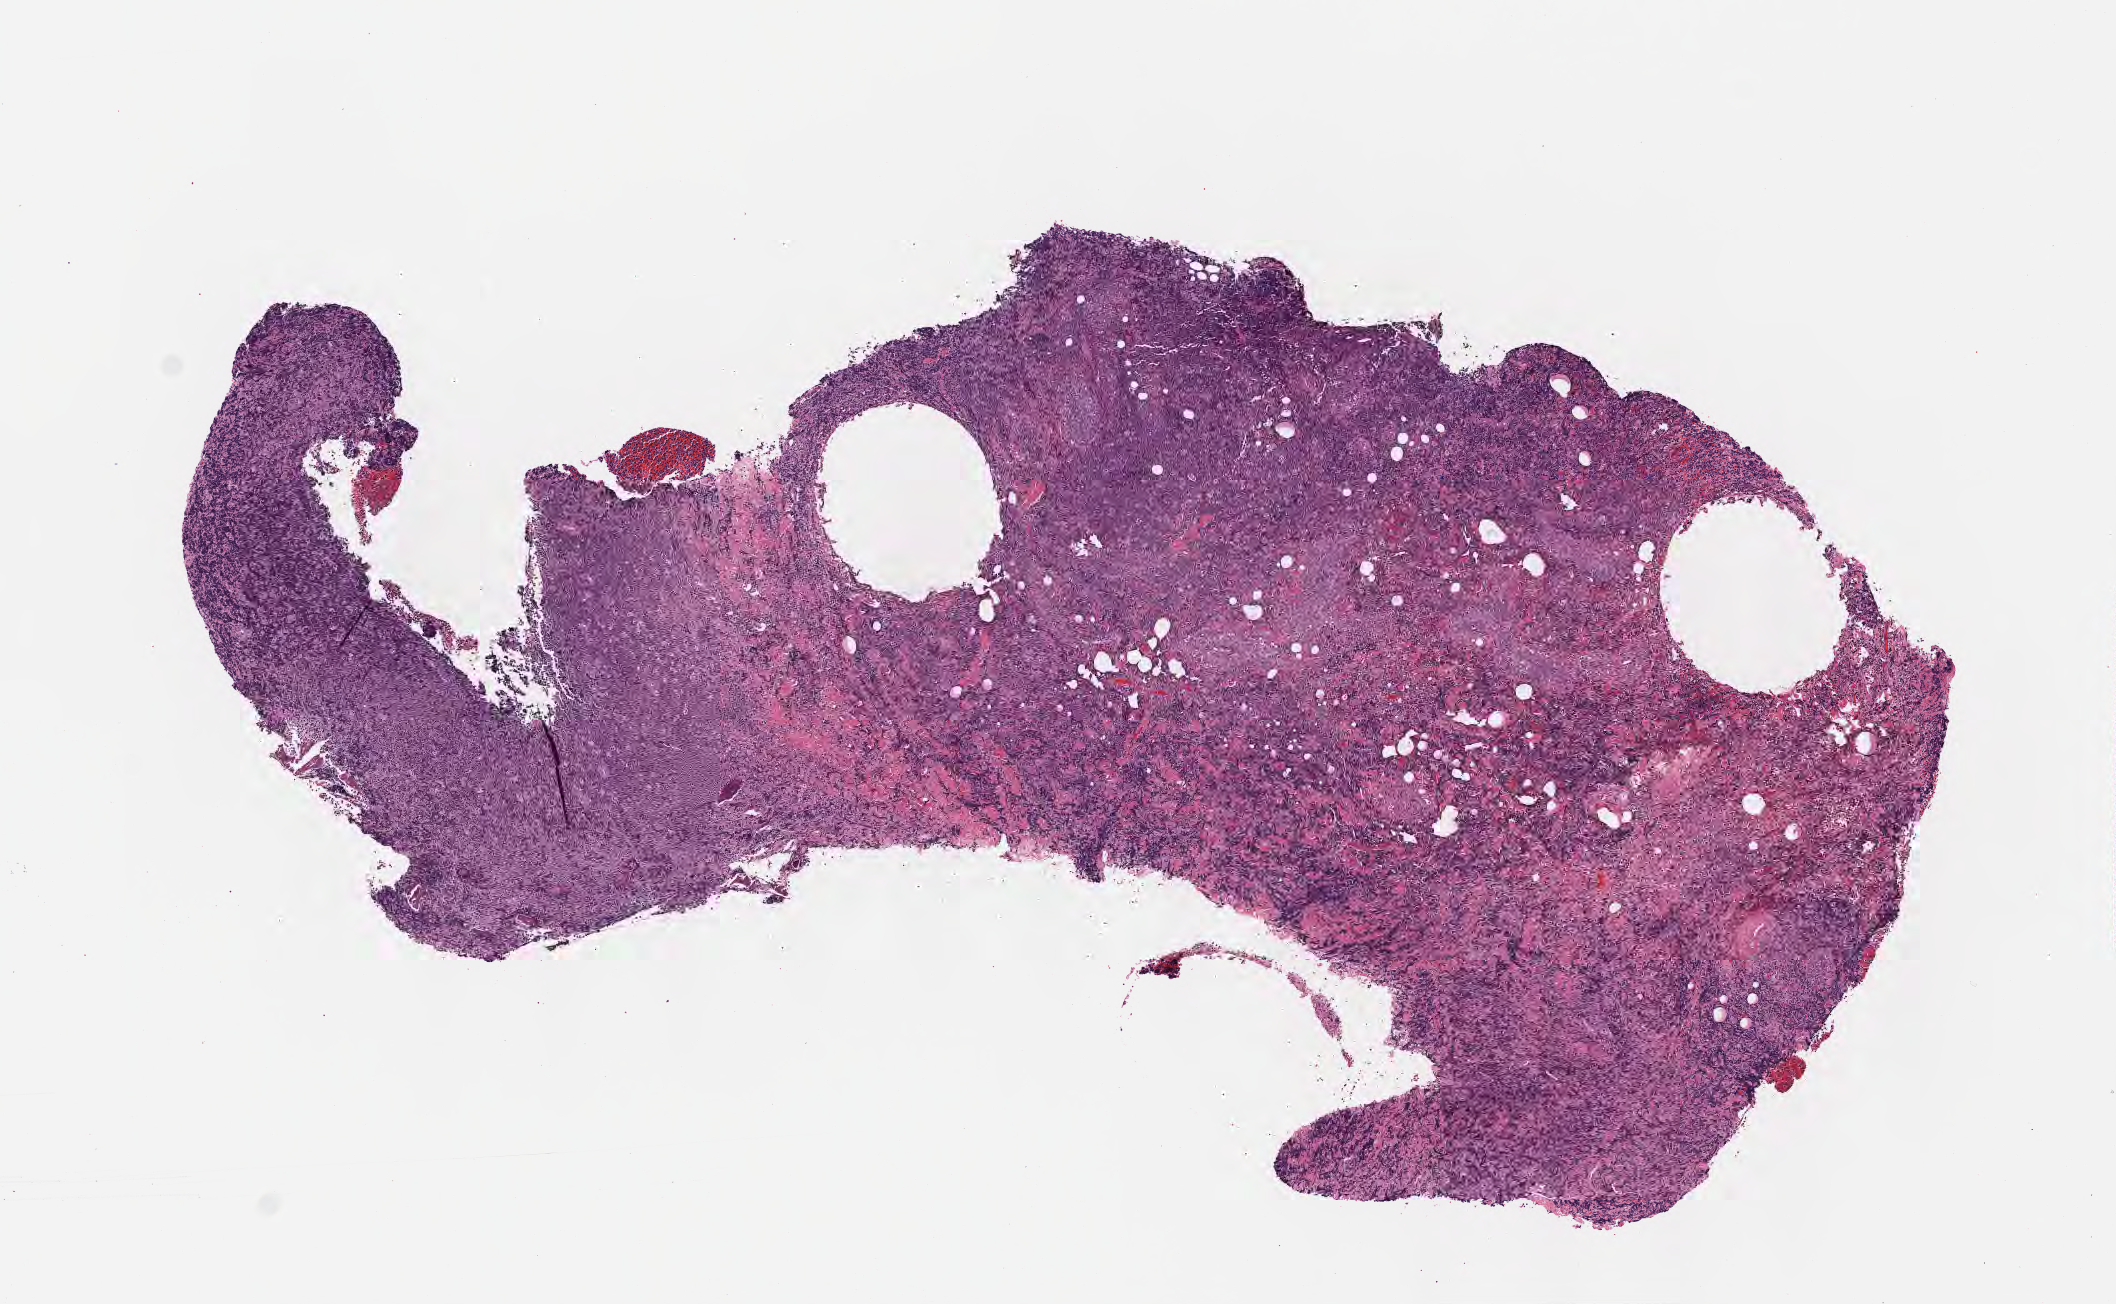
Digitized H&E-stained section, whole scanned area (about 8.6 x 5.3 mm) shown as a low-resolution overview. FFPE section. Primary tumor. Anatomic site: vestibule of mouth. Male, age 5 years at initial diagnosis. Pathologist review of this section (percent, as recorded): tumor cells 85%, tumor nuclei 90%, stromal cells 5%, necrosis 5%, normal cells 5%. Infiltration values recorded for this section: lymphocyte infiltration 40%, monocyte infiltration 30%, neutrophil infiltration 5%.
Histologic diagnosis: Diffuse large B-cell lymphoma, NOS. Ann Arbor stage (patient): Stage IV. Section: bottom of the tissue portion.